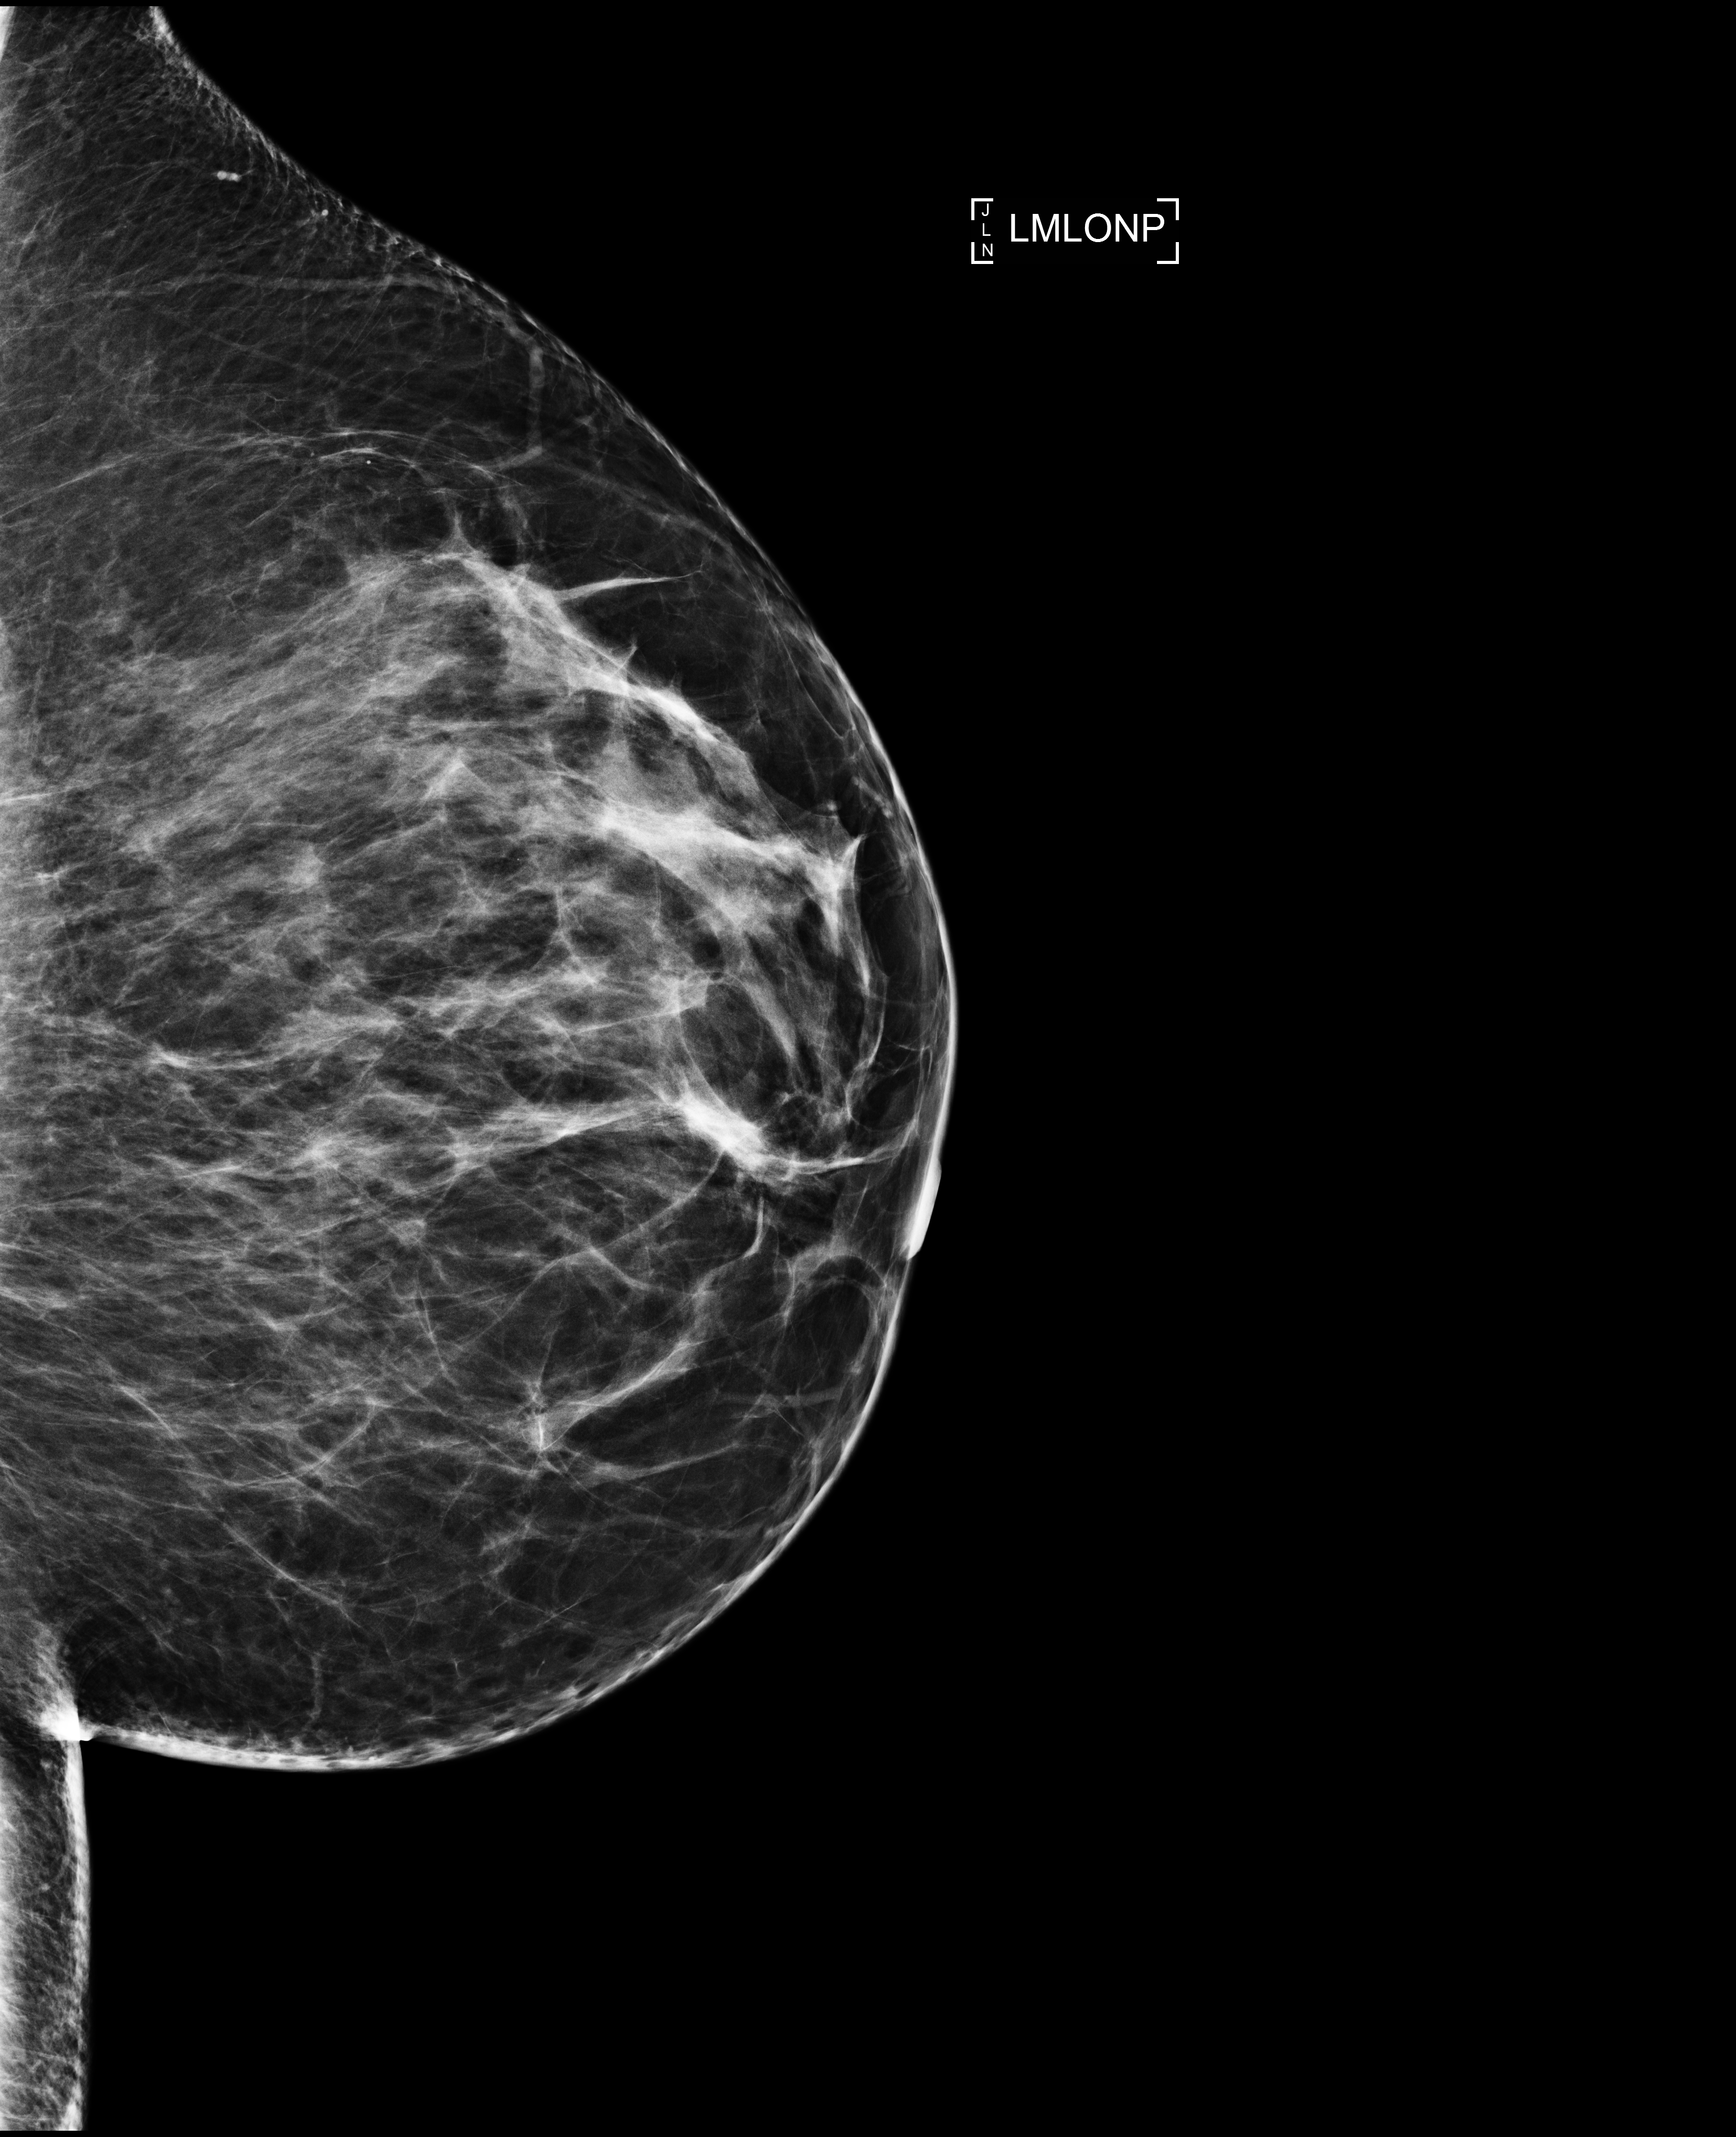
Annual screening mammography examination. Patient: female, 52 years.
Image type: full-field digital mammogram. Breast: left. Projection: mediolateral oblique (MLO) view, nipple in profile.